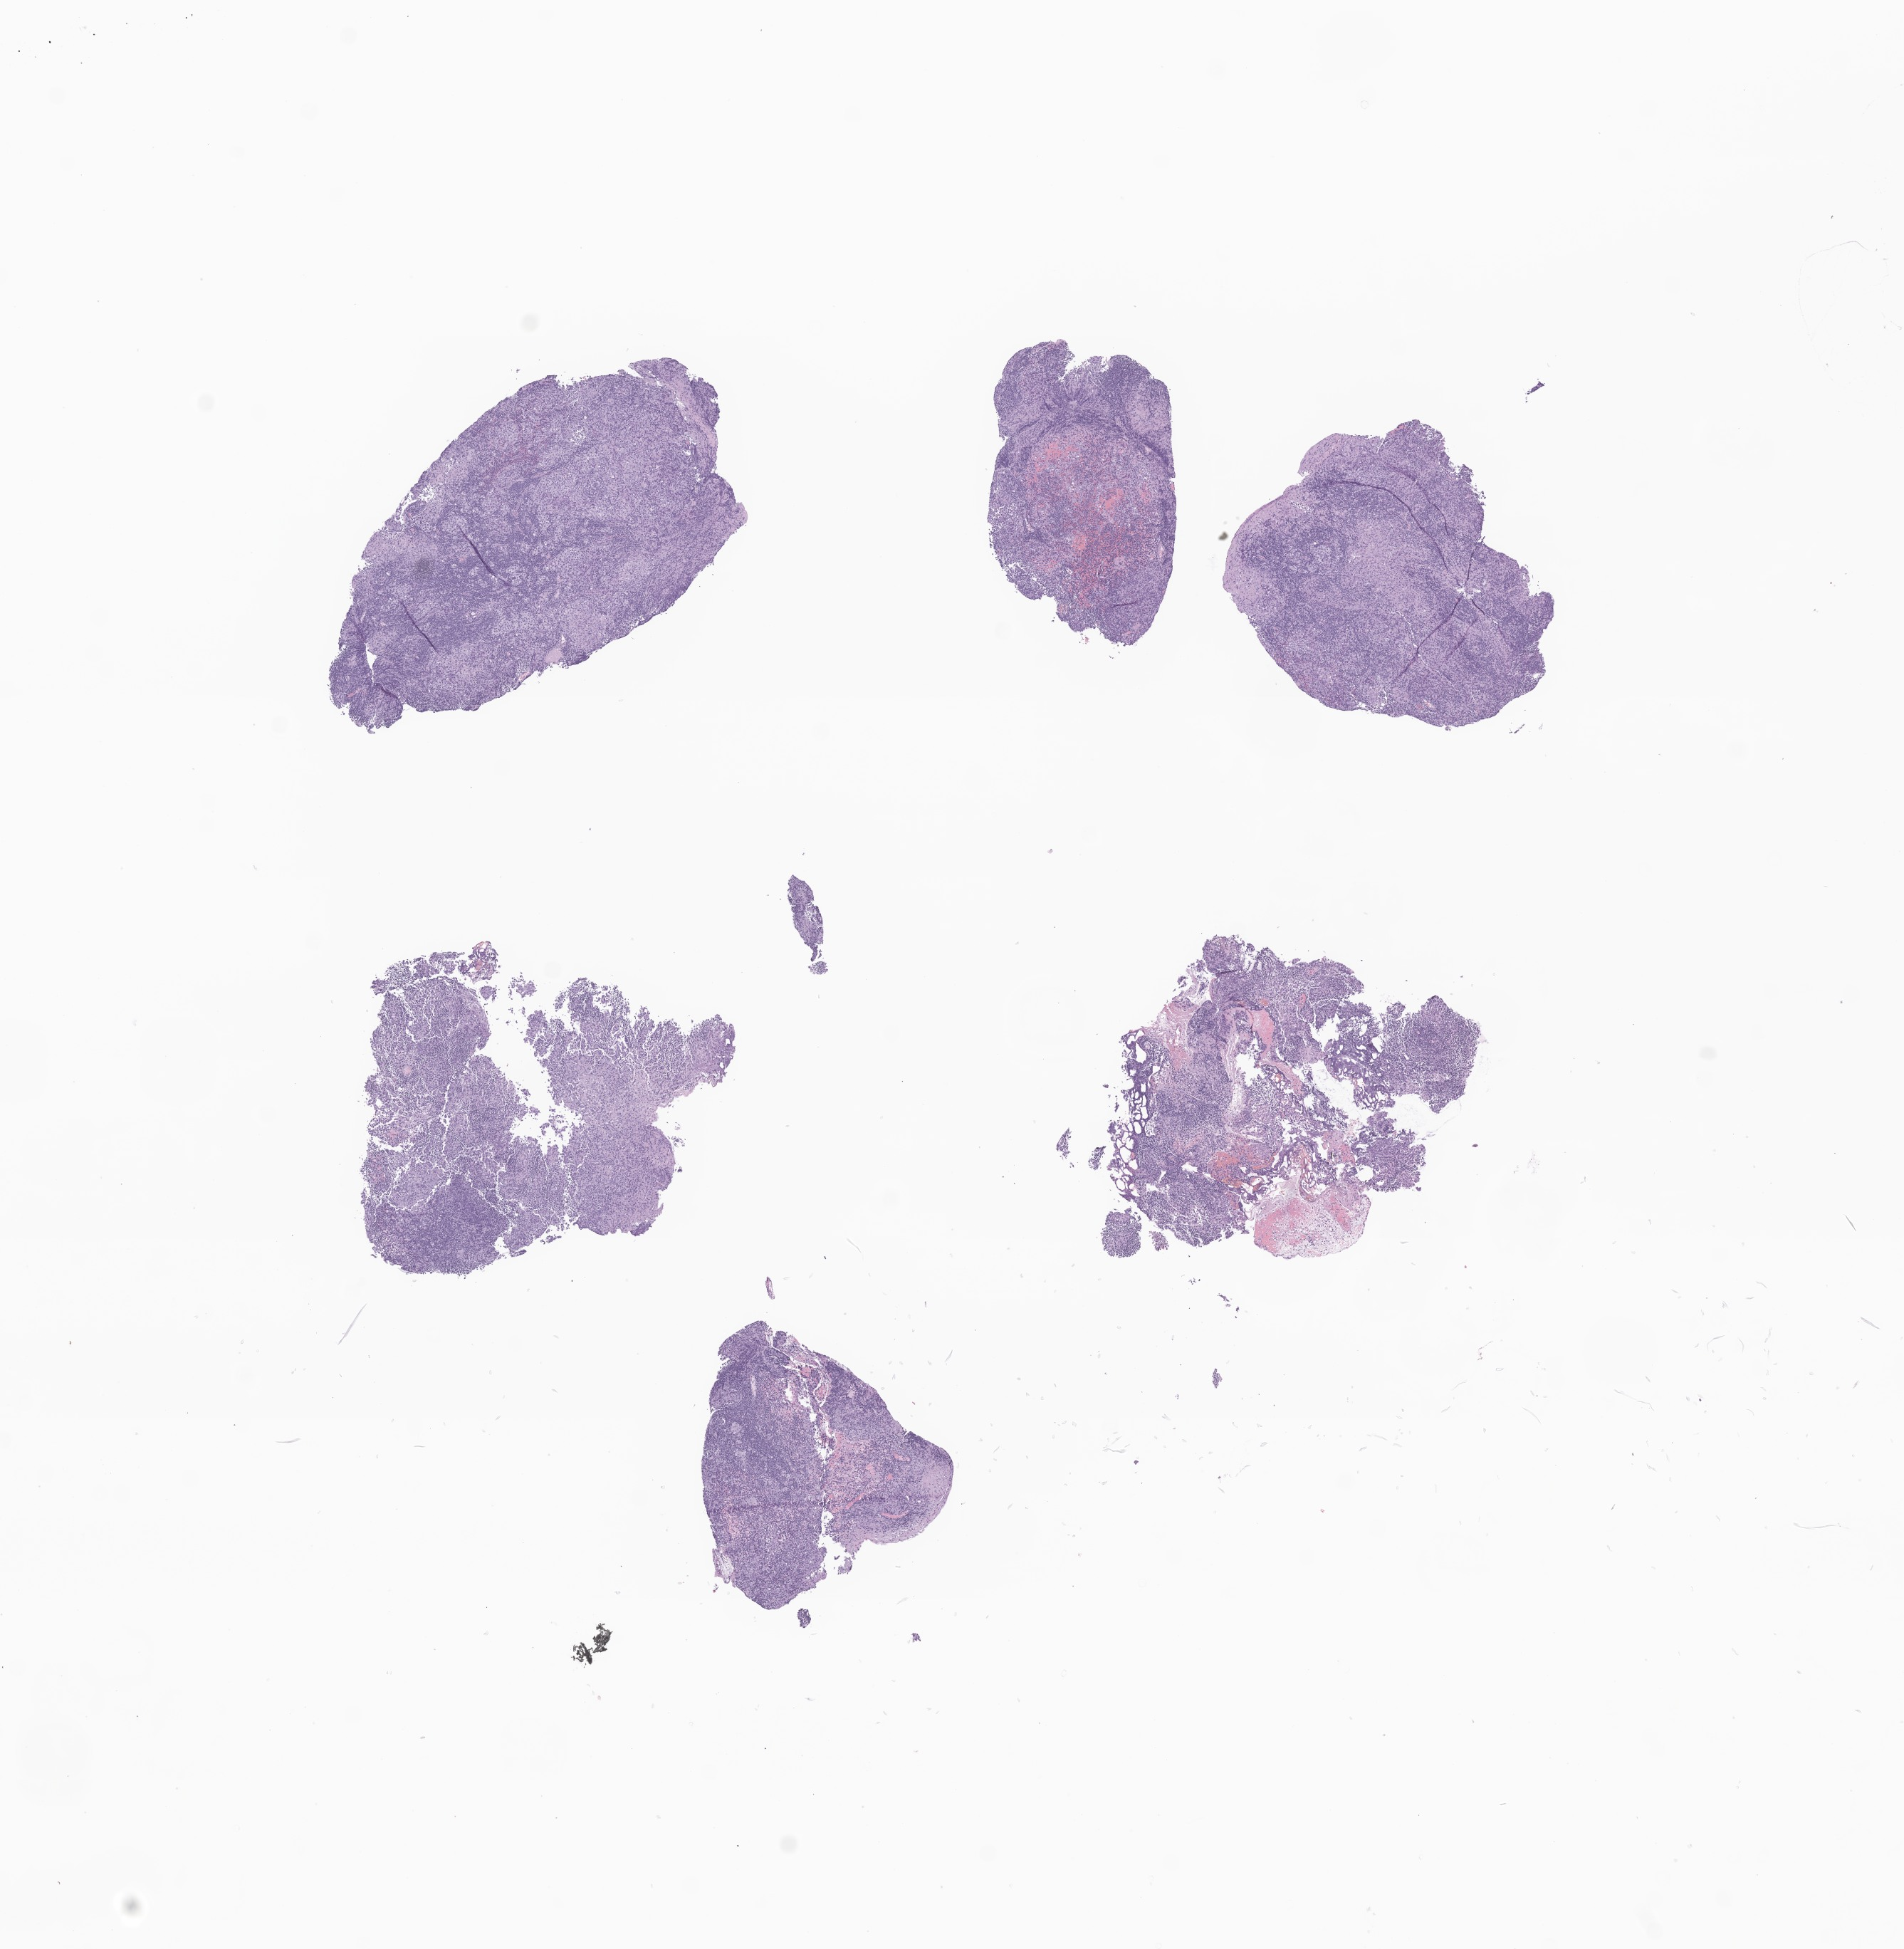
Digitized haematoxylin and eosin-stained section of tumor tissue from the pineal gland — low-resolution overview of the scanned area, about 11.3 x 11.5 mm, formalin-fixed, paraffin-embedded (FFPE) tissue. Patient male; age 192 months (16 years).
Recorded diagnosis: Germinoma.